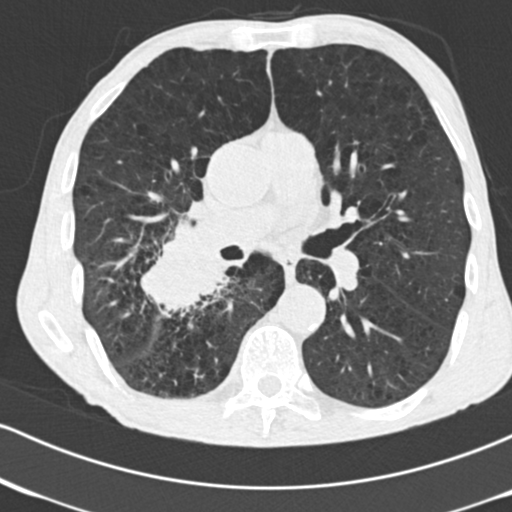
Low-dose screening chest CT, one axial slice; reconstruction kernel B30f; 120 kVp; lung window (W 1500 / L -600 HU); 2 mm slice thickness; 512 × 512 image matrix, field of view 316 × 316 mm.
Structures marked on this image (manually delineated by an expert):
- lesion 1 (tumor, lower lobe of right lung): box from (x=140, y=224) to (x=227, y=312) px